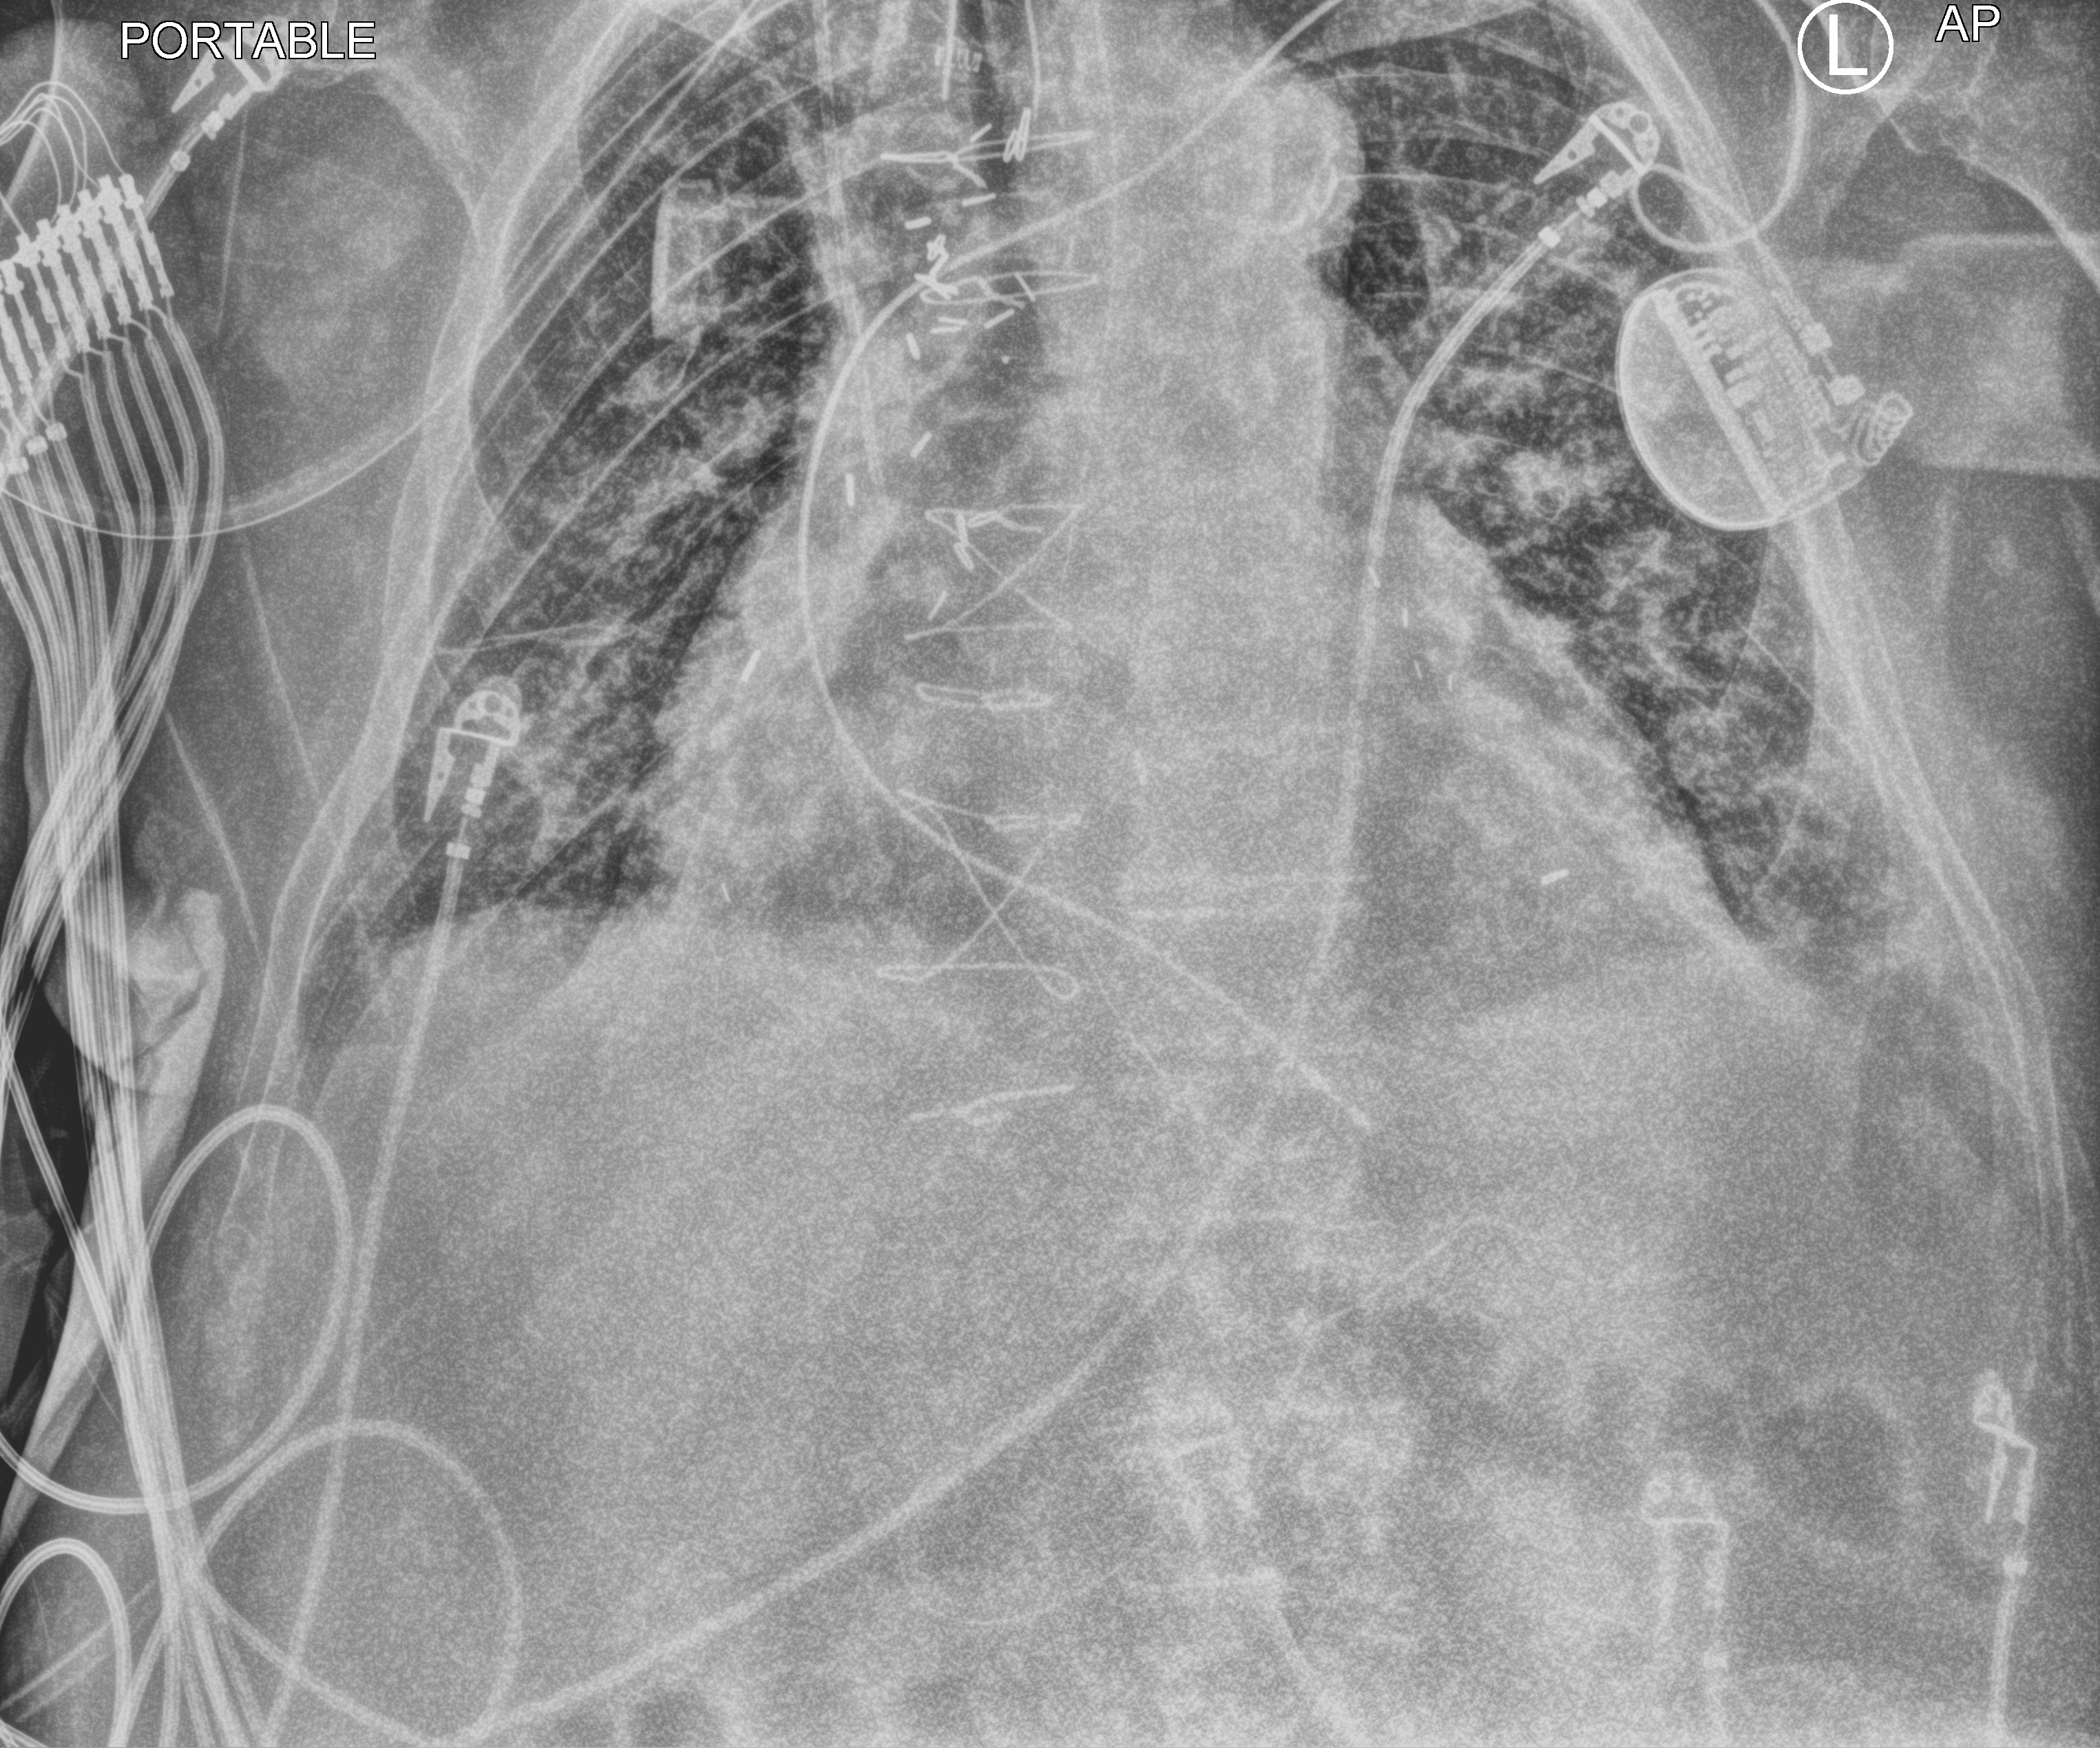
Bedside chest radiograph (computed radiography). Male patient hospitalised with COVID-19, age 75–90 years.
From the hospital-stay record, not from the radiograph (when in the stay this image was taken is not recorded): length of hospital stay: 16 days.